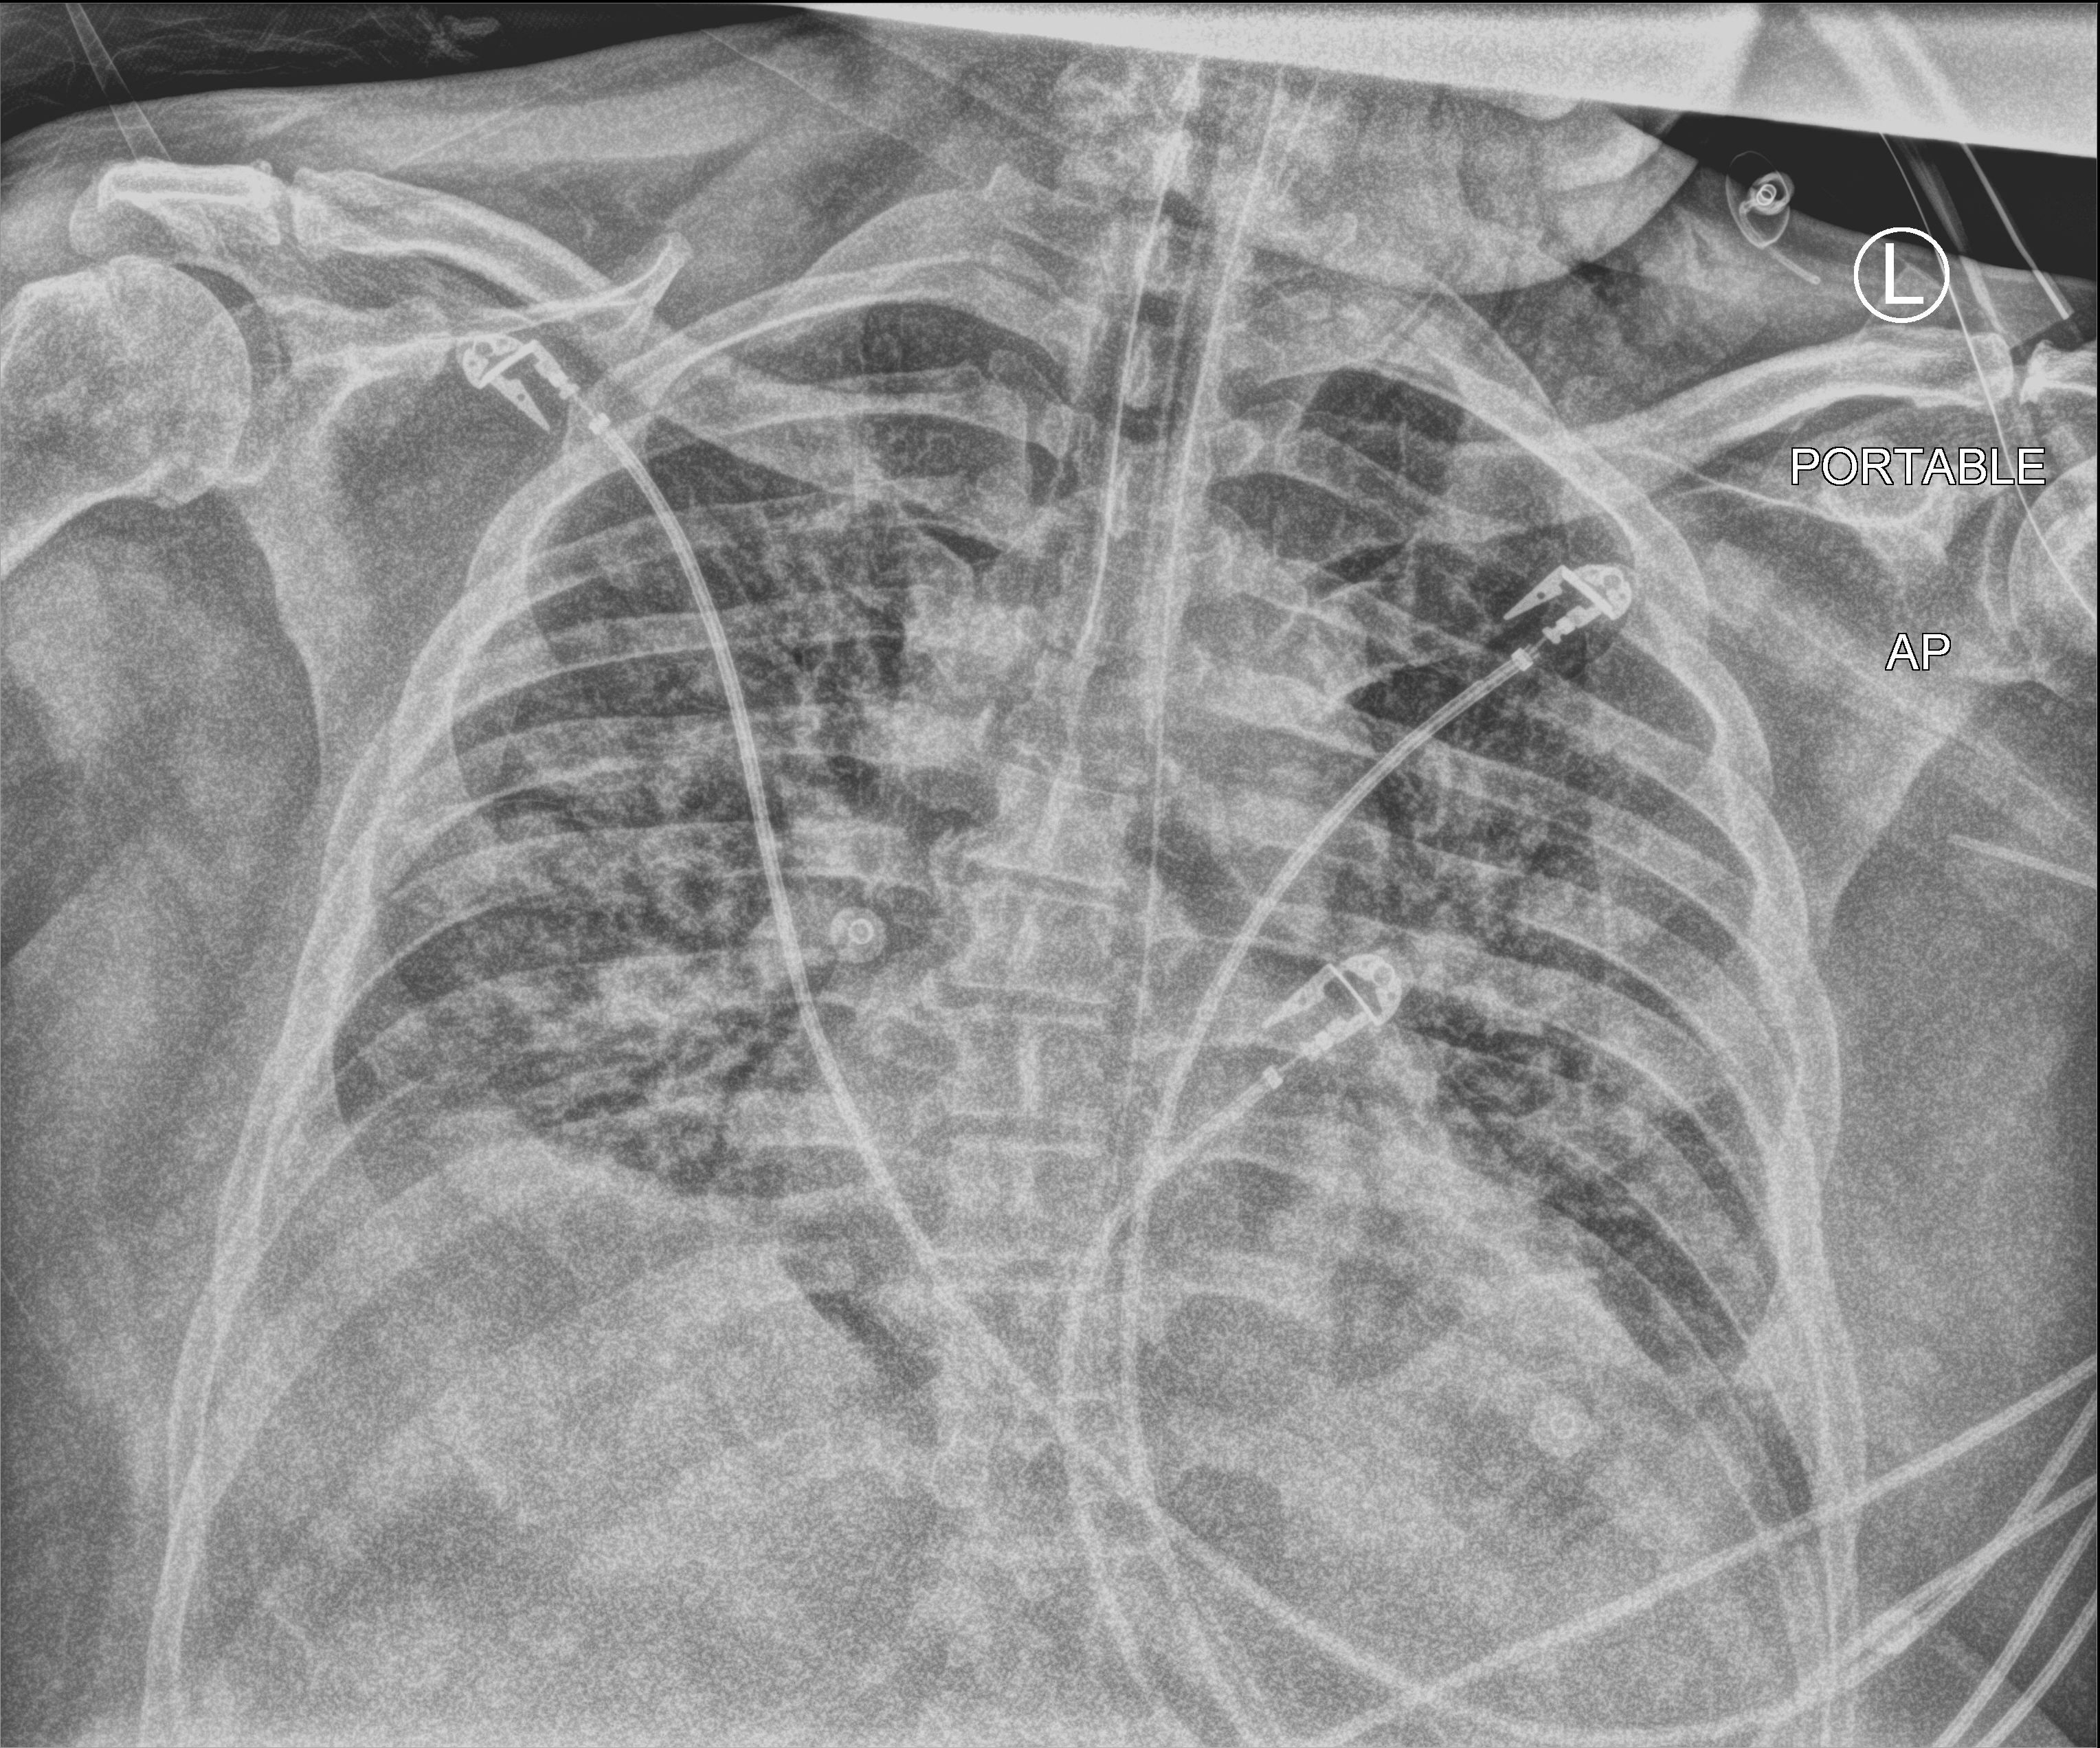
Bedside chest radiograph (computed radiography), anteroposterior (AP) projection. Patient hospitalised with COVID-19; male, aged 18–59 years.
Admission-level facts for this patient (not findings on this image; timing relative to this image not recorded): length of hospital stay: 22 days; admitted to intensive care during this hospital stay: yes; other chronic lung disease (admission record): yes.